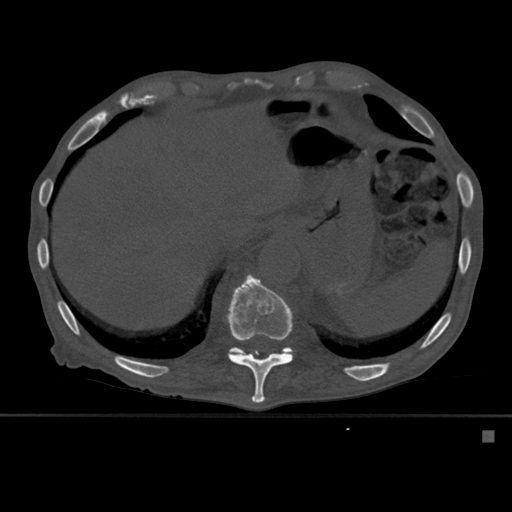
CT including the spine, one axial slice. Slice 292 of 527 in the series (ordered by position). Bone window (W 1800 / L 400 HU). 512 × 512 image matrix, field of view 373 × 373 mm. Male patient, age 78 years. From the clinical record (not read from this slice): primary cancer: prostate.
Outlined on this slice (semi-automatic segmentation, software-assisted and operator-edited):
- T11 vertebra: bounding box [x1, y1, x2, y2] px = [226, 274, 293, 403]
- T12 vertebra: [228, 347, 293, 358]